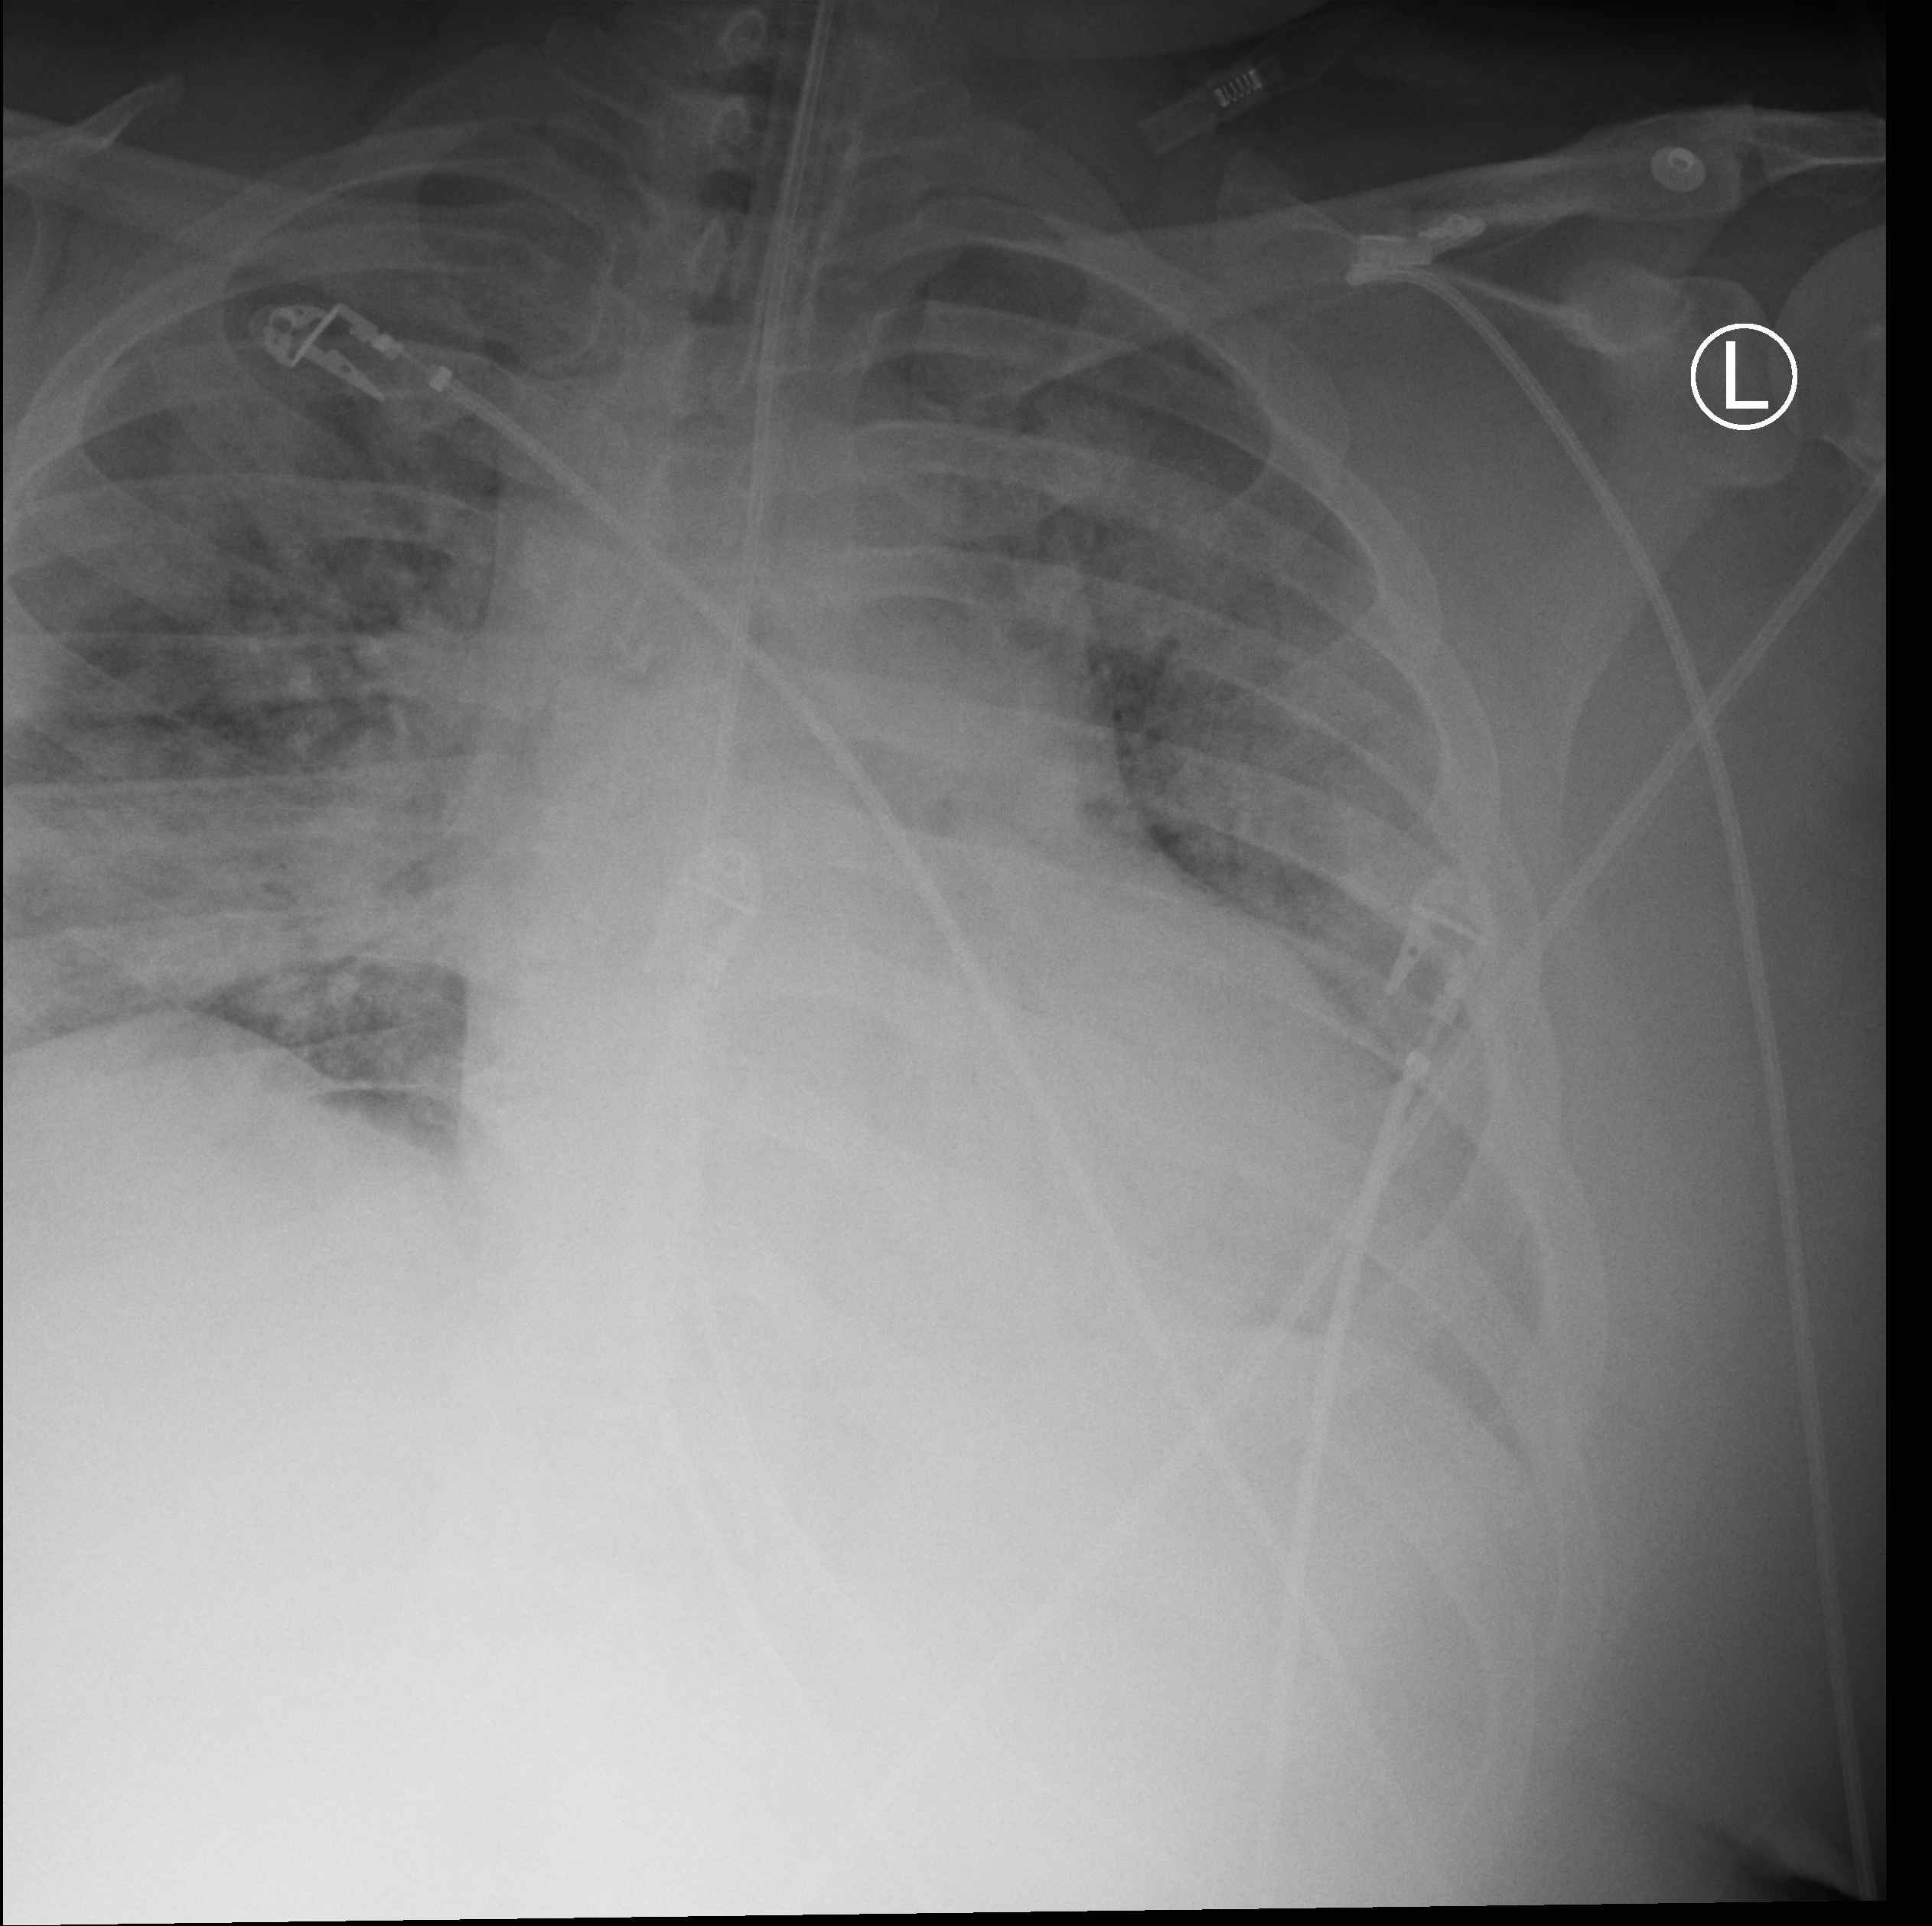
Bedside chest radiograph (computed radiography). Adult patient hospitalised with COVID-19, age 18–59 years.
From the hospital-stay record, not from the radiograph (when in the stay this image was taken is not recorded):
- length of hospital stay: 10 days
- mechanically ventilated during this hospital stay: yes
- admitted to intensive care during this hospital stay: yes